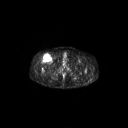
FDG PET of an extremity soft-tissue mass (from a PET/CT study), one axial slice; slice 304 of 311 in the series (ordered by position); 3.27 mm slice thickness; 128 × 128 image matrix, field of view 700 × 700 mm. Patient: male, 56 years. From the clinical record (not read from this slice): histological type: pleiomorphic leiomyosarcoma; grade: intermediate; site of the primary tumour: right thigh.
Annotated regions visible in this slice (expert contour drawn on MRI and transferred to this co-registered scan by the dataset authors):
- gross tumour volume including surrounding oedema: bounding box [x1, y1, x2, y2] px = [42, 54, 51, 63]
- gross tumour volume (mass): [43, 55, 51, 63]